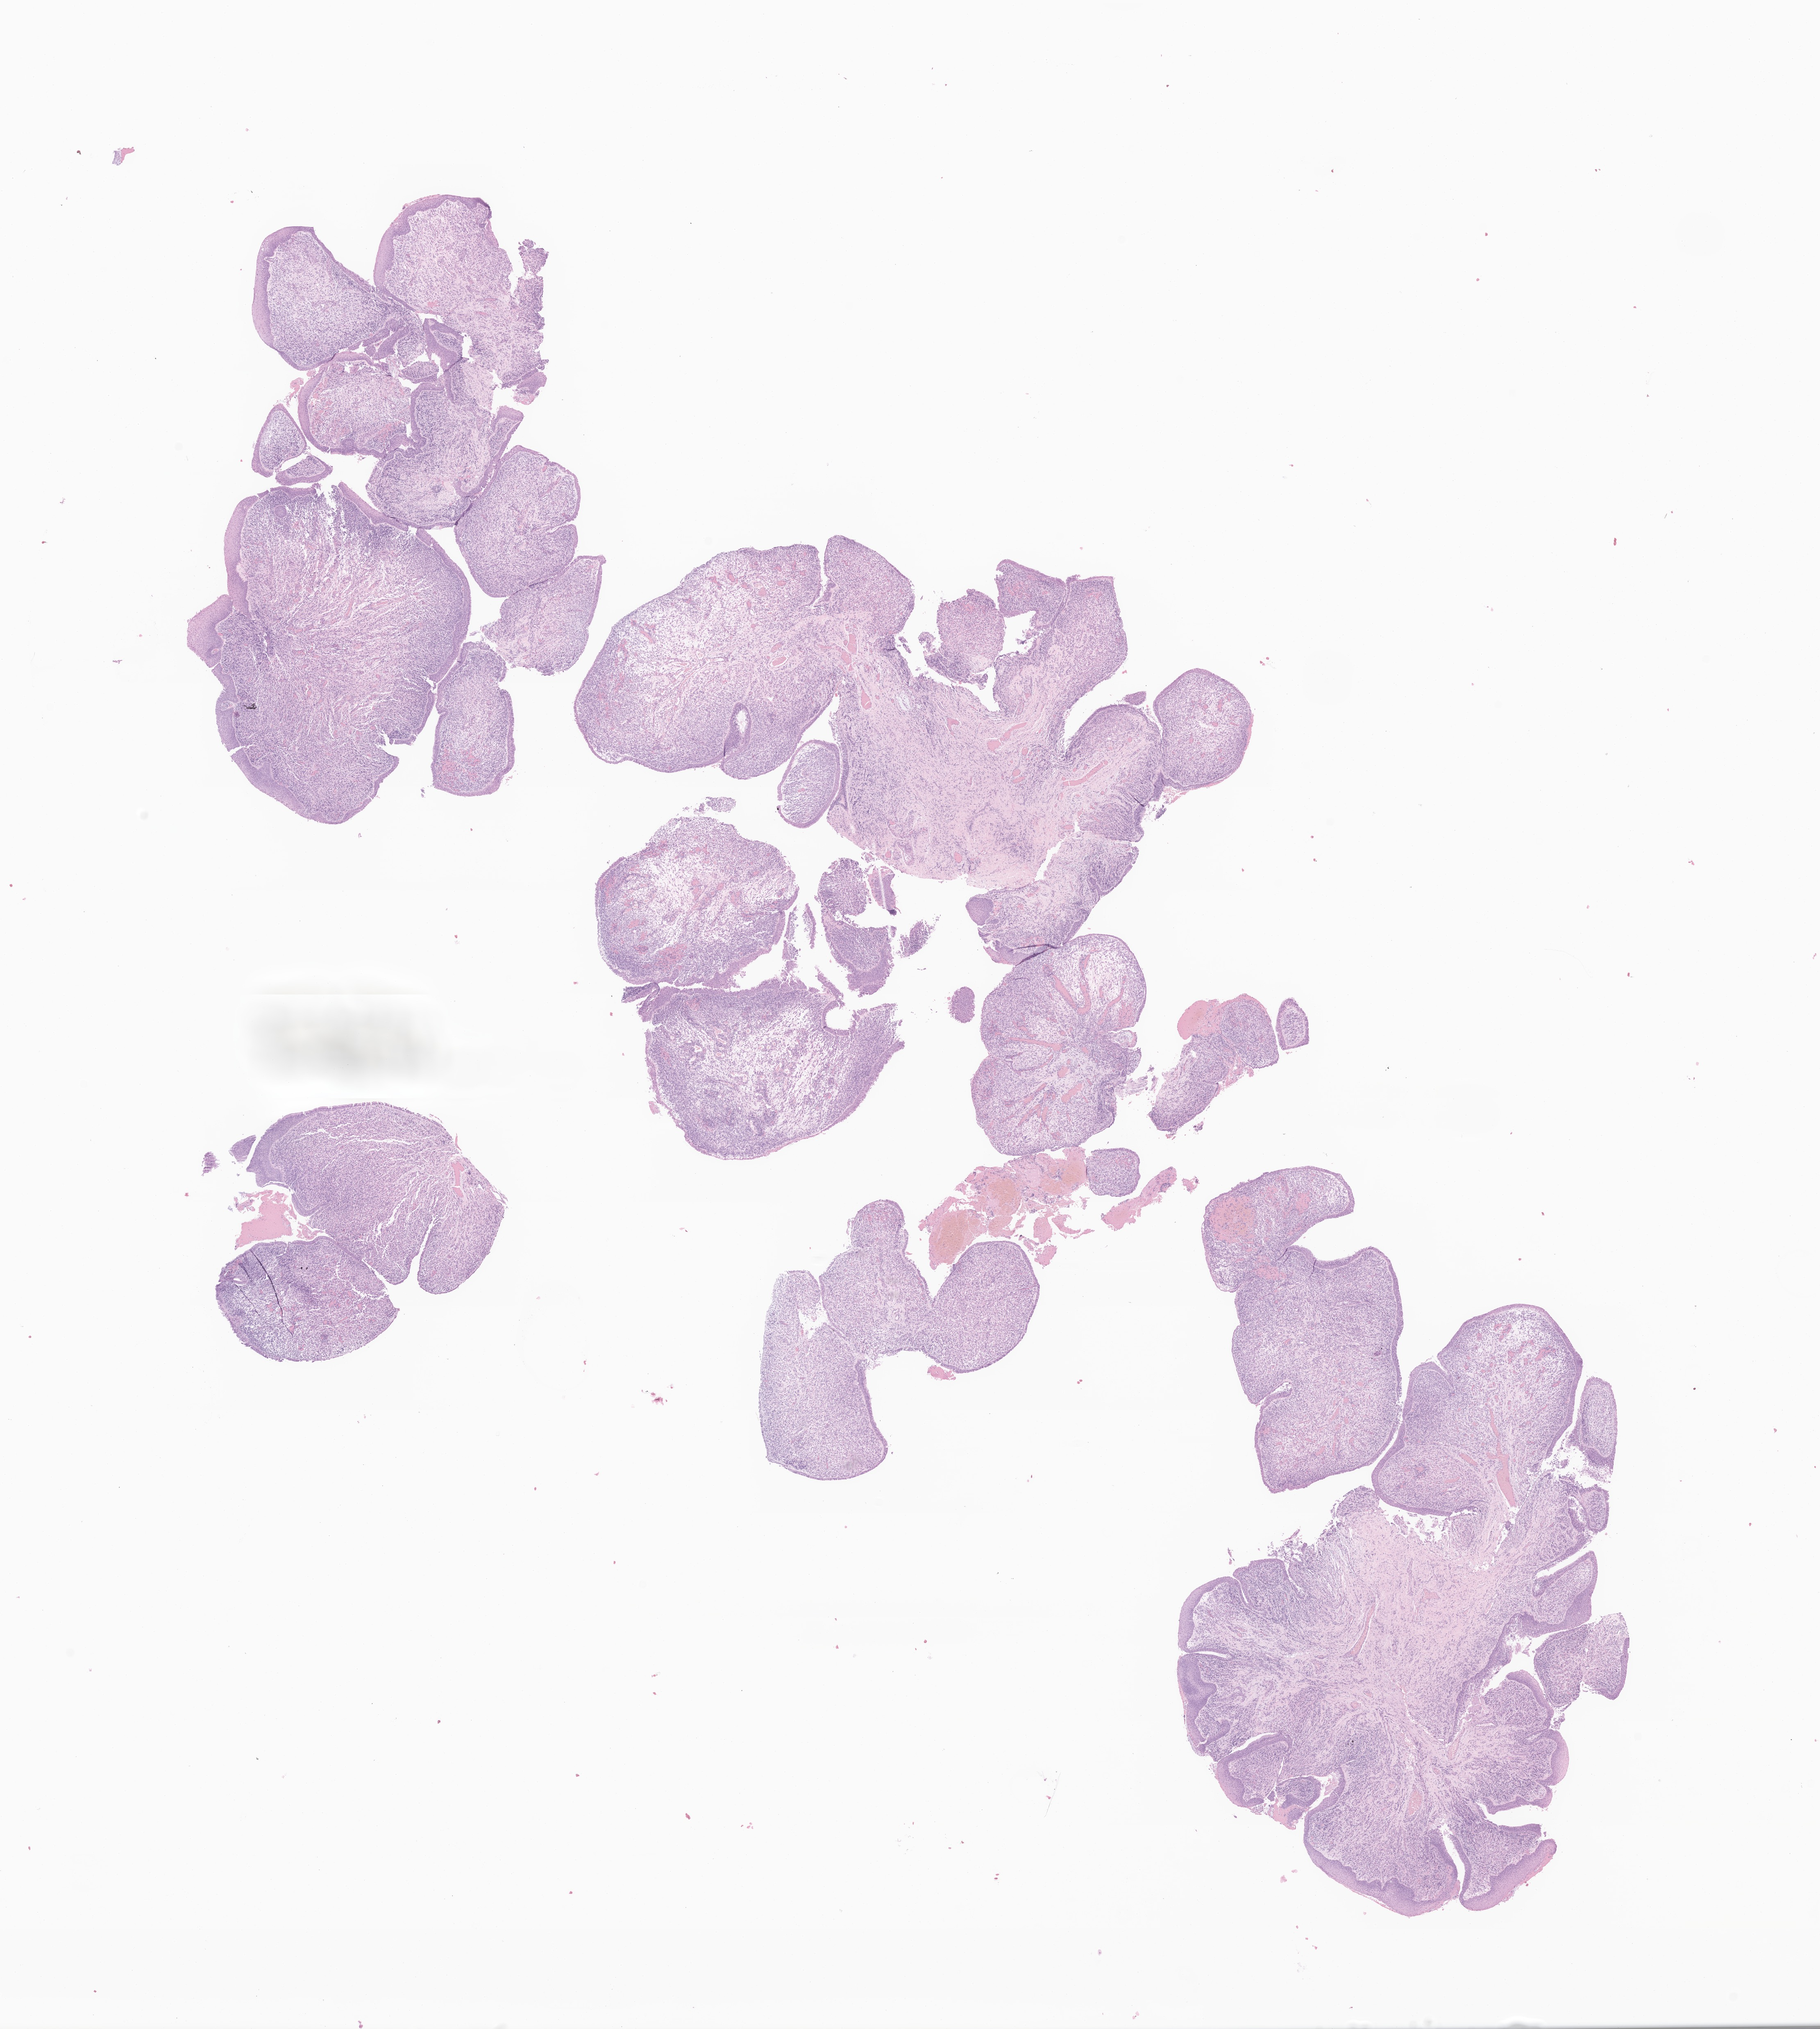
H&E whole-slide image of tumor tissue from the nasal cavity, low-resolution overview of the scanned area, about 18.7 x 20.9 mm. Formalin-fixed, paraffin-embedded (FFPE) tissue. Female patient, age 42 months (3 years 6 months).
Diagnosis: Embryonal rhabdomyosarcoma, NOS.